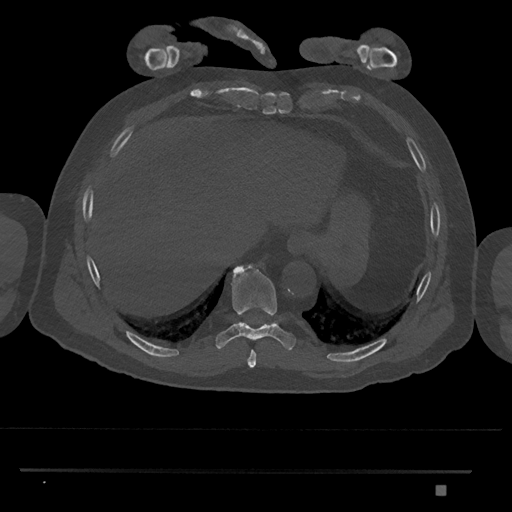
CT including the spine, one axial slice; position 1055 of 1134 along the scan axis; reconstruction kernel Br40s/3; 120 kVp; bone window (W 1800 / L 400 HU); 0.5 mm slice thickness; 512 × 512 image matrix, field of view 429 × 429 mm. Male patient, age 65 years. Case-level facts recorded for this patient, not image findings: primary cancer: prostate.
Outlined on this slice (semi-automatically segmented with operator editing):
- T10 vertebra: bounding box <274,321,278,322> (left, top, right, bottom; pixels)
- T8 vertebra: <247,350,257,367>
- T9 vertebra: <216,263,297,350>